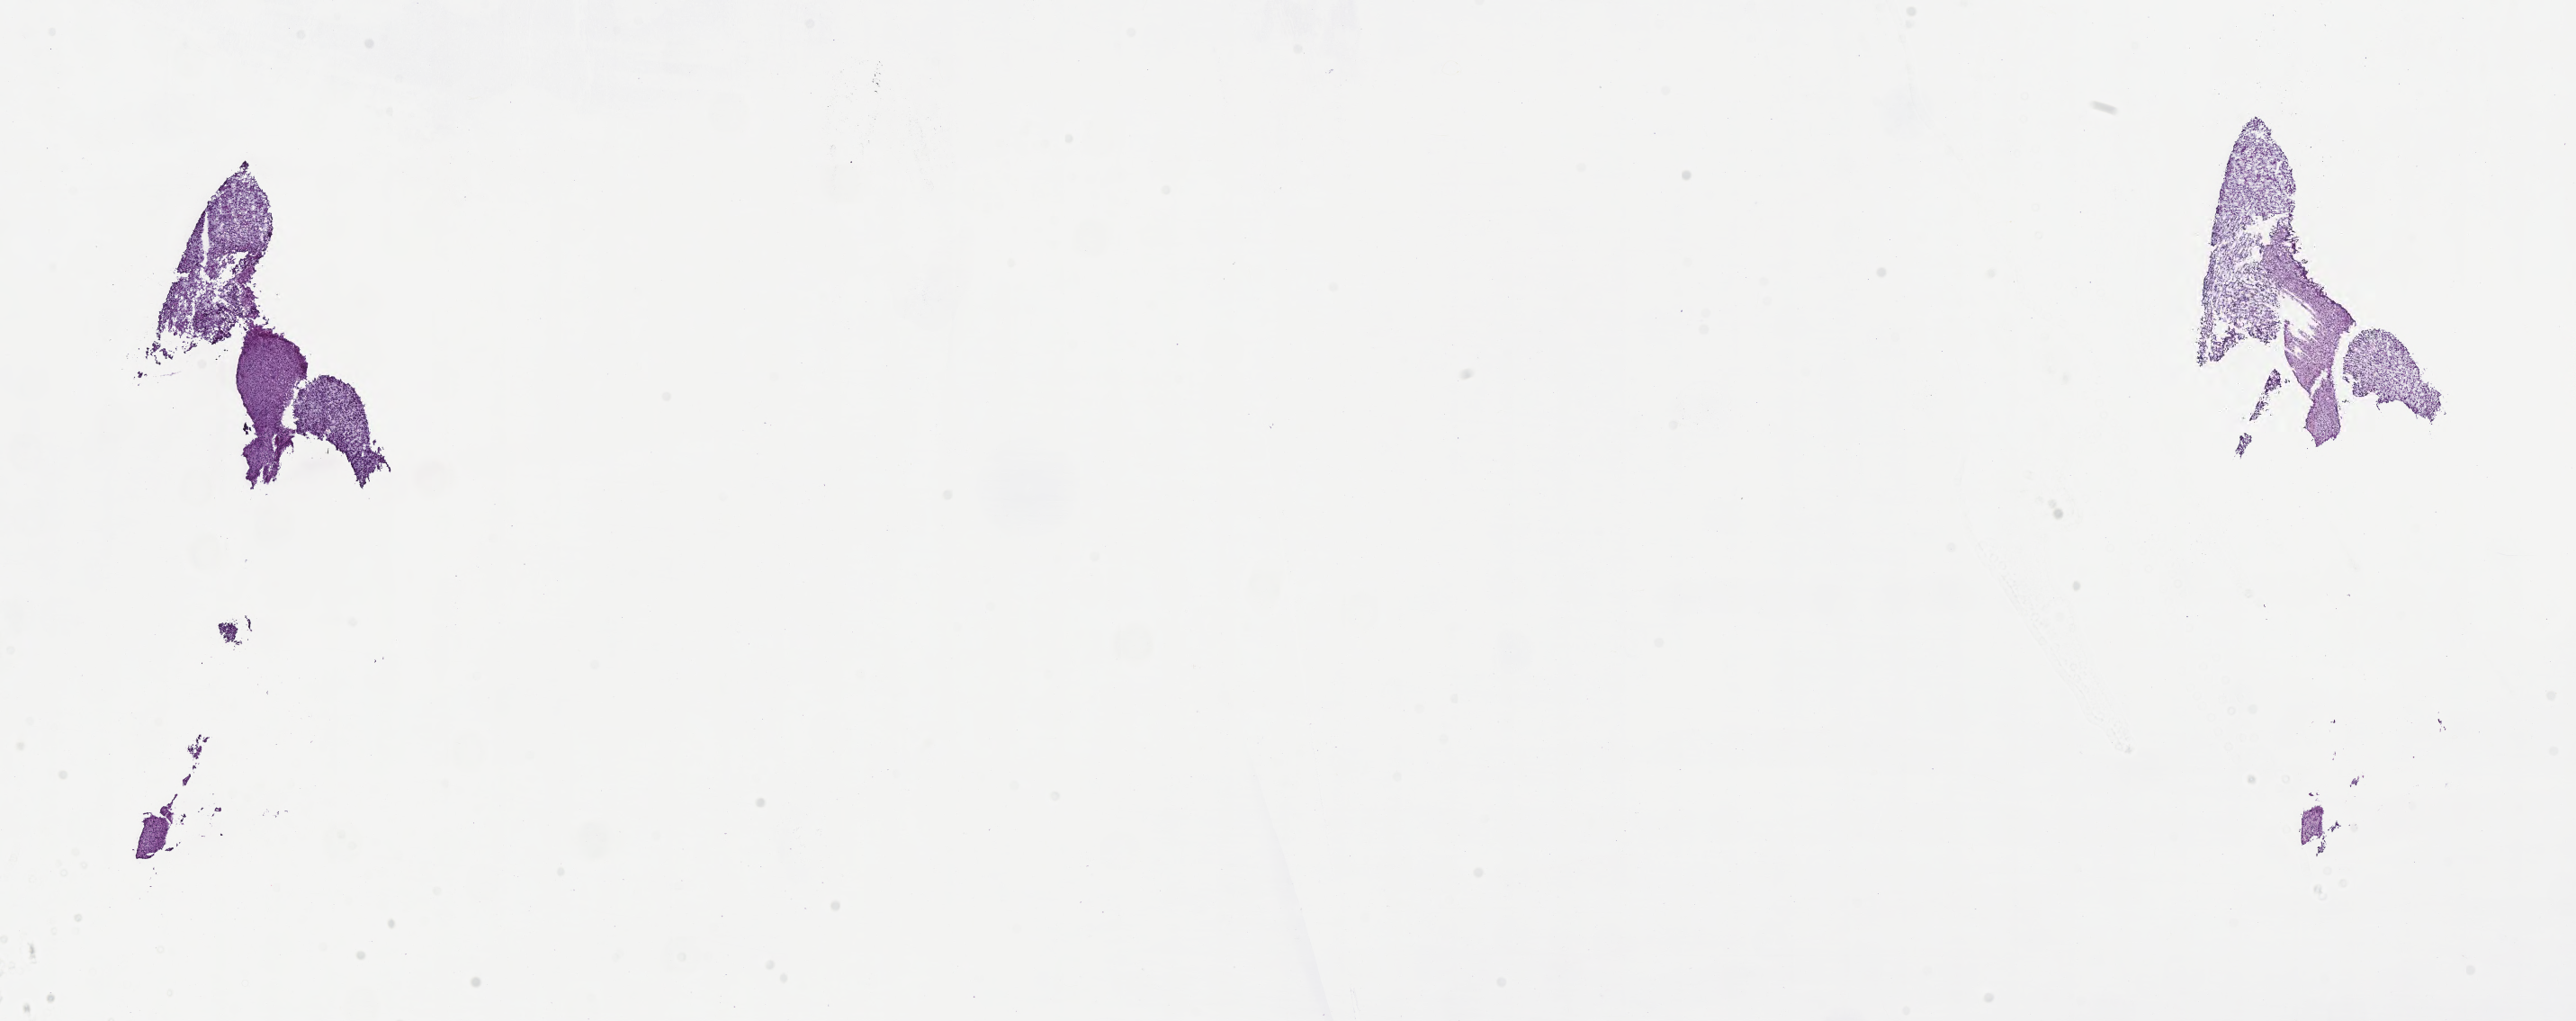
Whole-slide image, H&E stain of tumor tissue from the brain, whole scanned area (about 23.1 x 9.2 mm) shown as a low-resolution overview, frozen section (OCT-embedded). Patient female; age 195 months (16 years 3 months).
- diagnosis: Neoplasm, uncertain whether benign or malignant